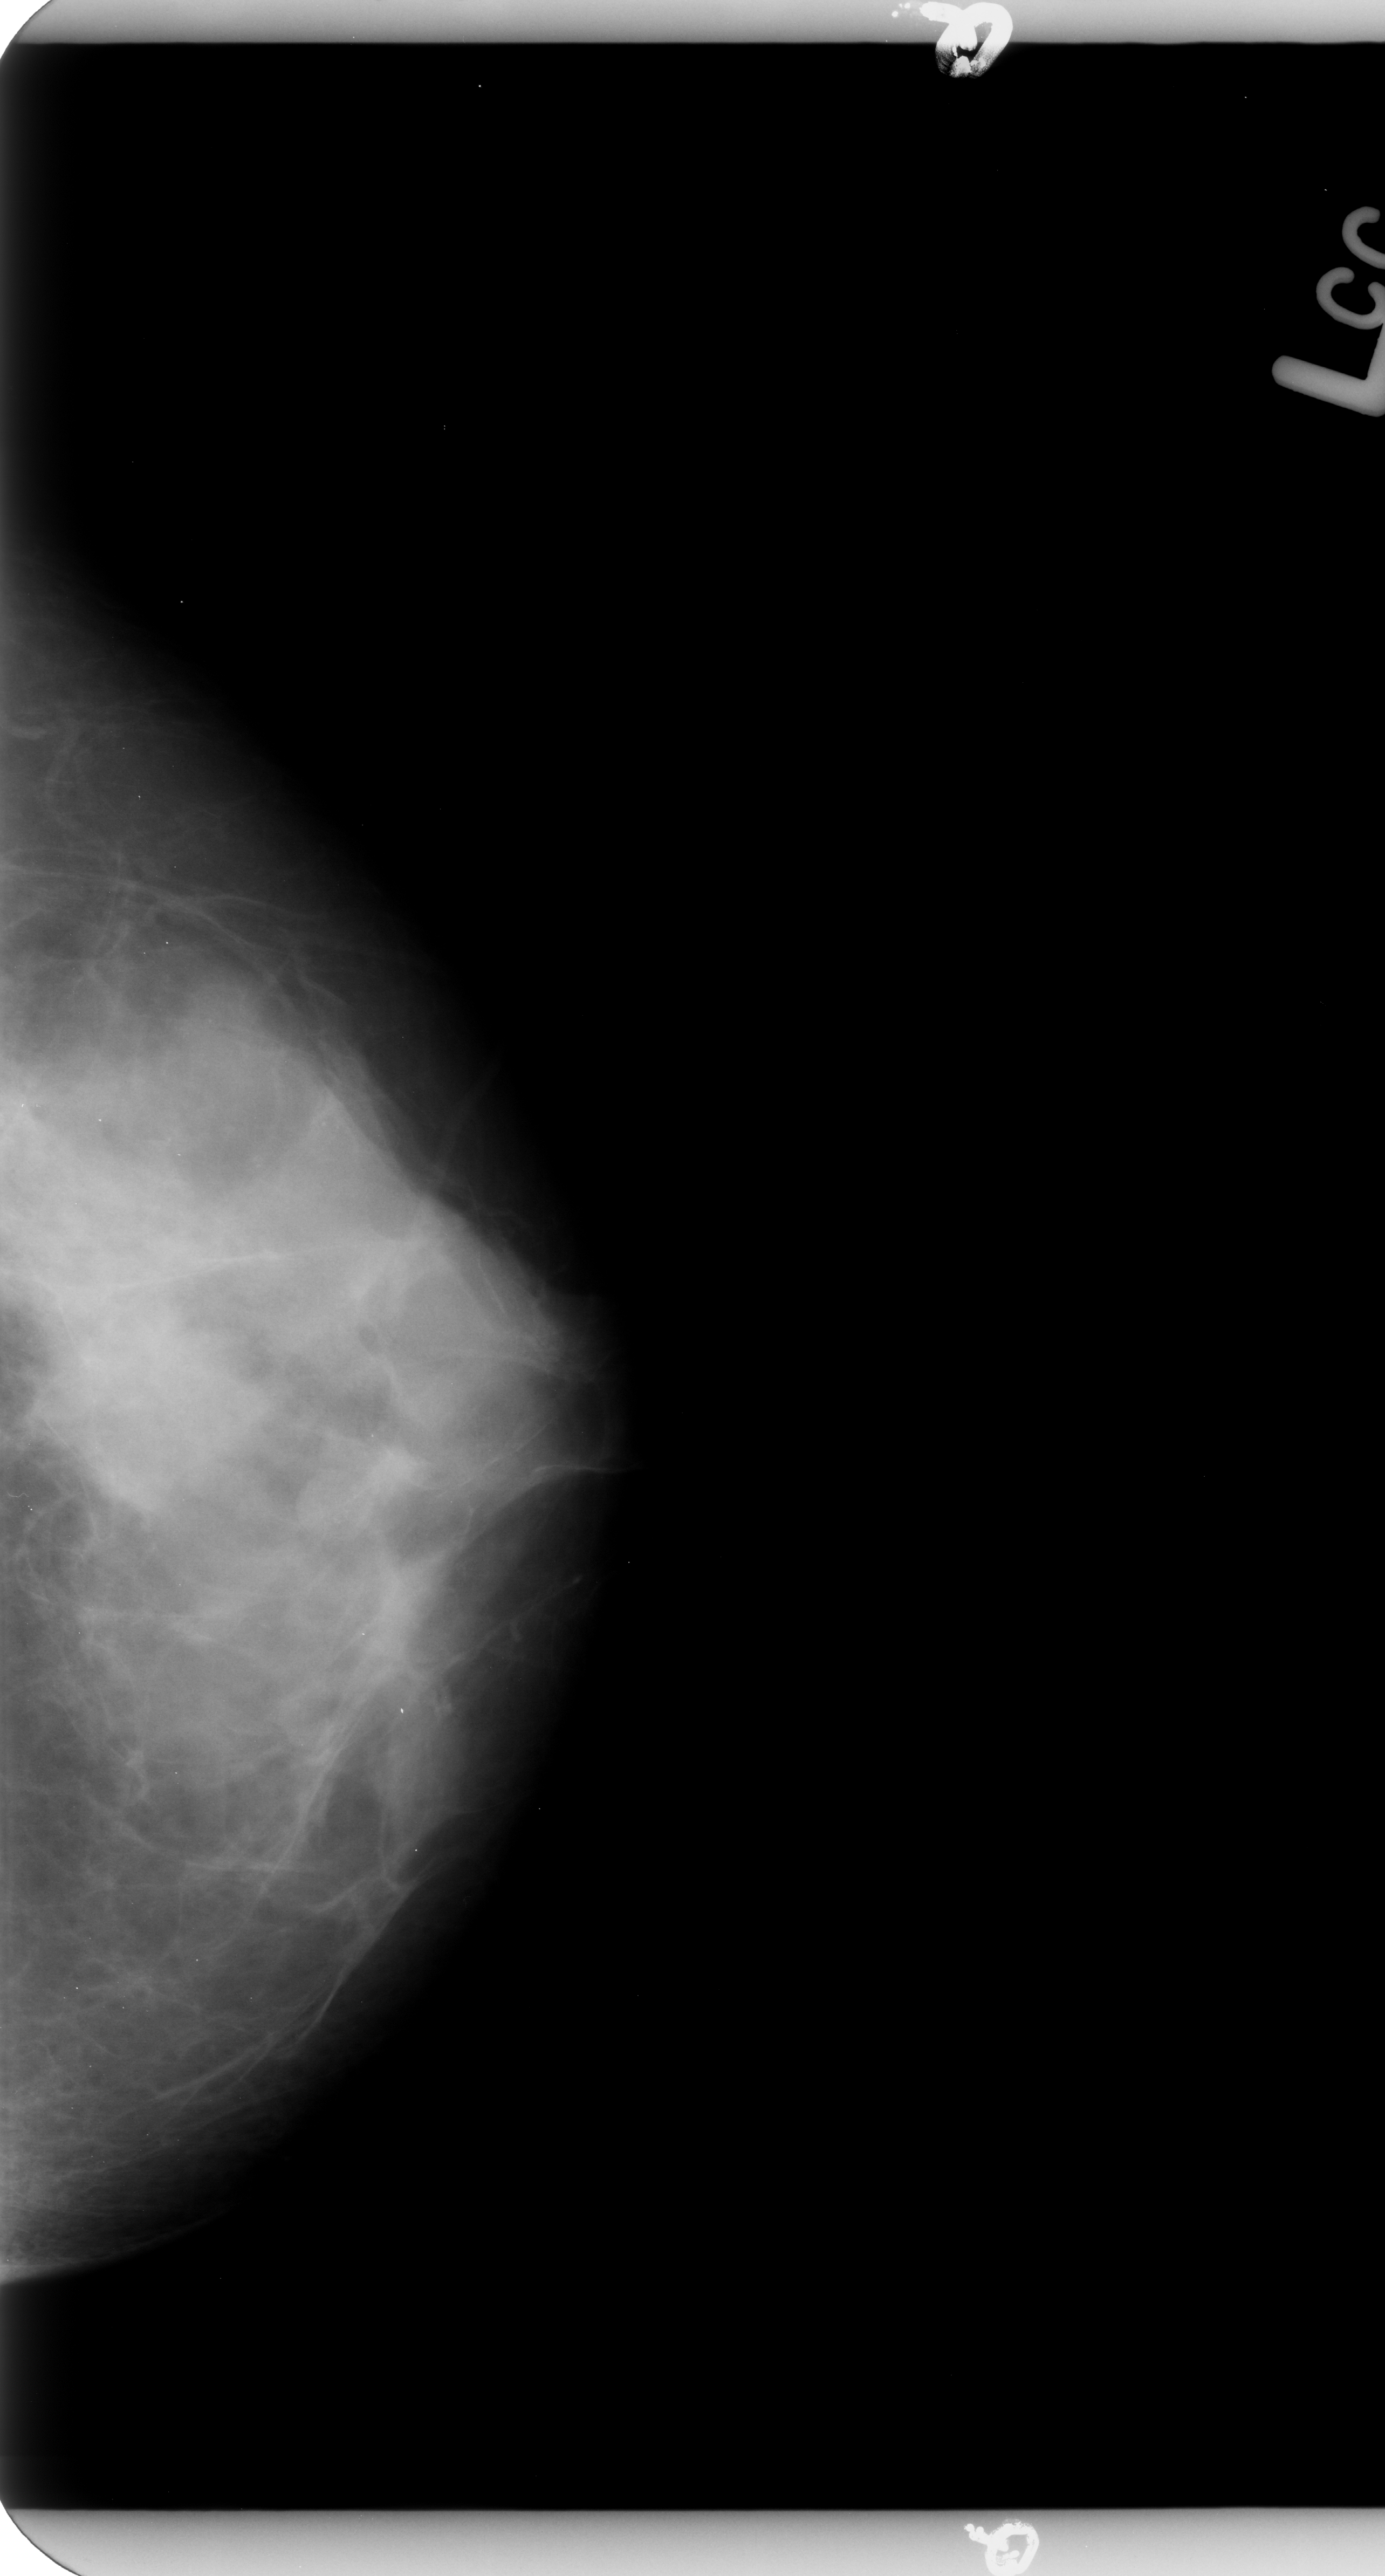
Scanned film-screen mammogram. Left breast. Craniocaudal (CC) view. BI-RADS breast density category 4 (scale 1–4). 1385 × 2576 image matrix.
Expert-marked regions of interest on this film, with their recorded descriptors:
- mass, shape round, margins circumscribed; BI-RADS assessment category 3; pathology result (as recorded, not read from the image): benign: bounding box (x1, y1, x2, y2) in pixels: (279, 1435, 421, 1547)